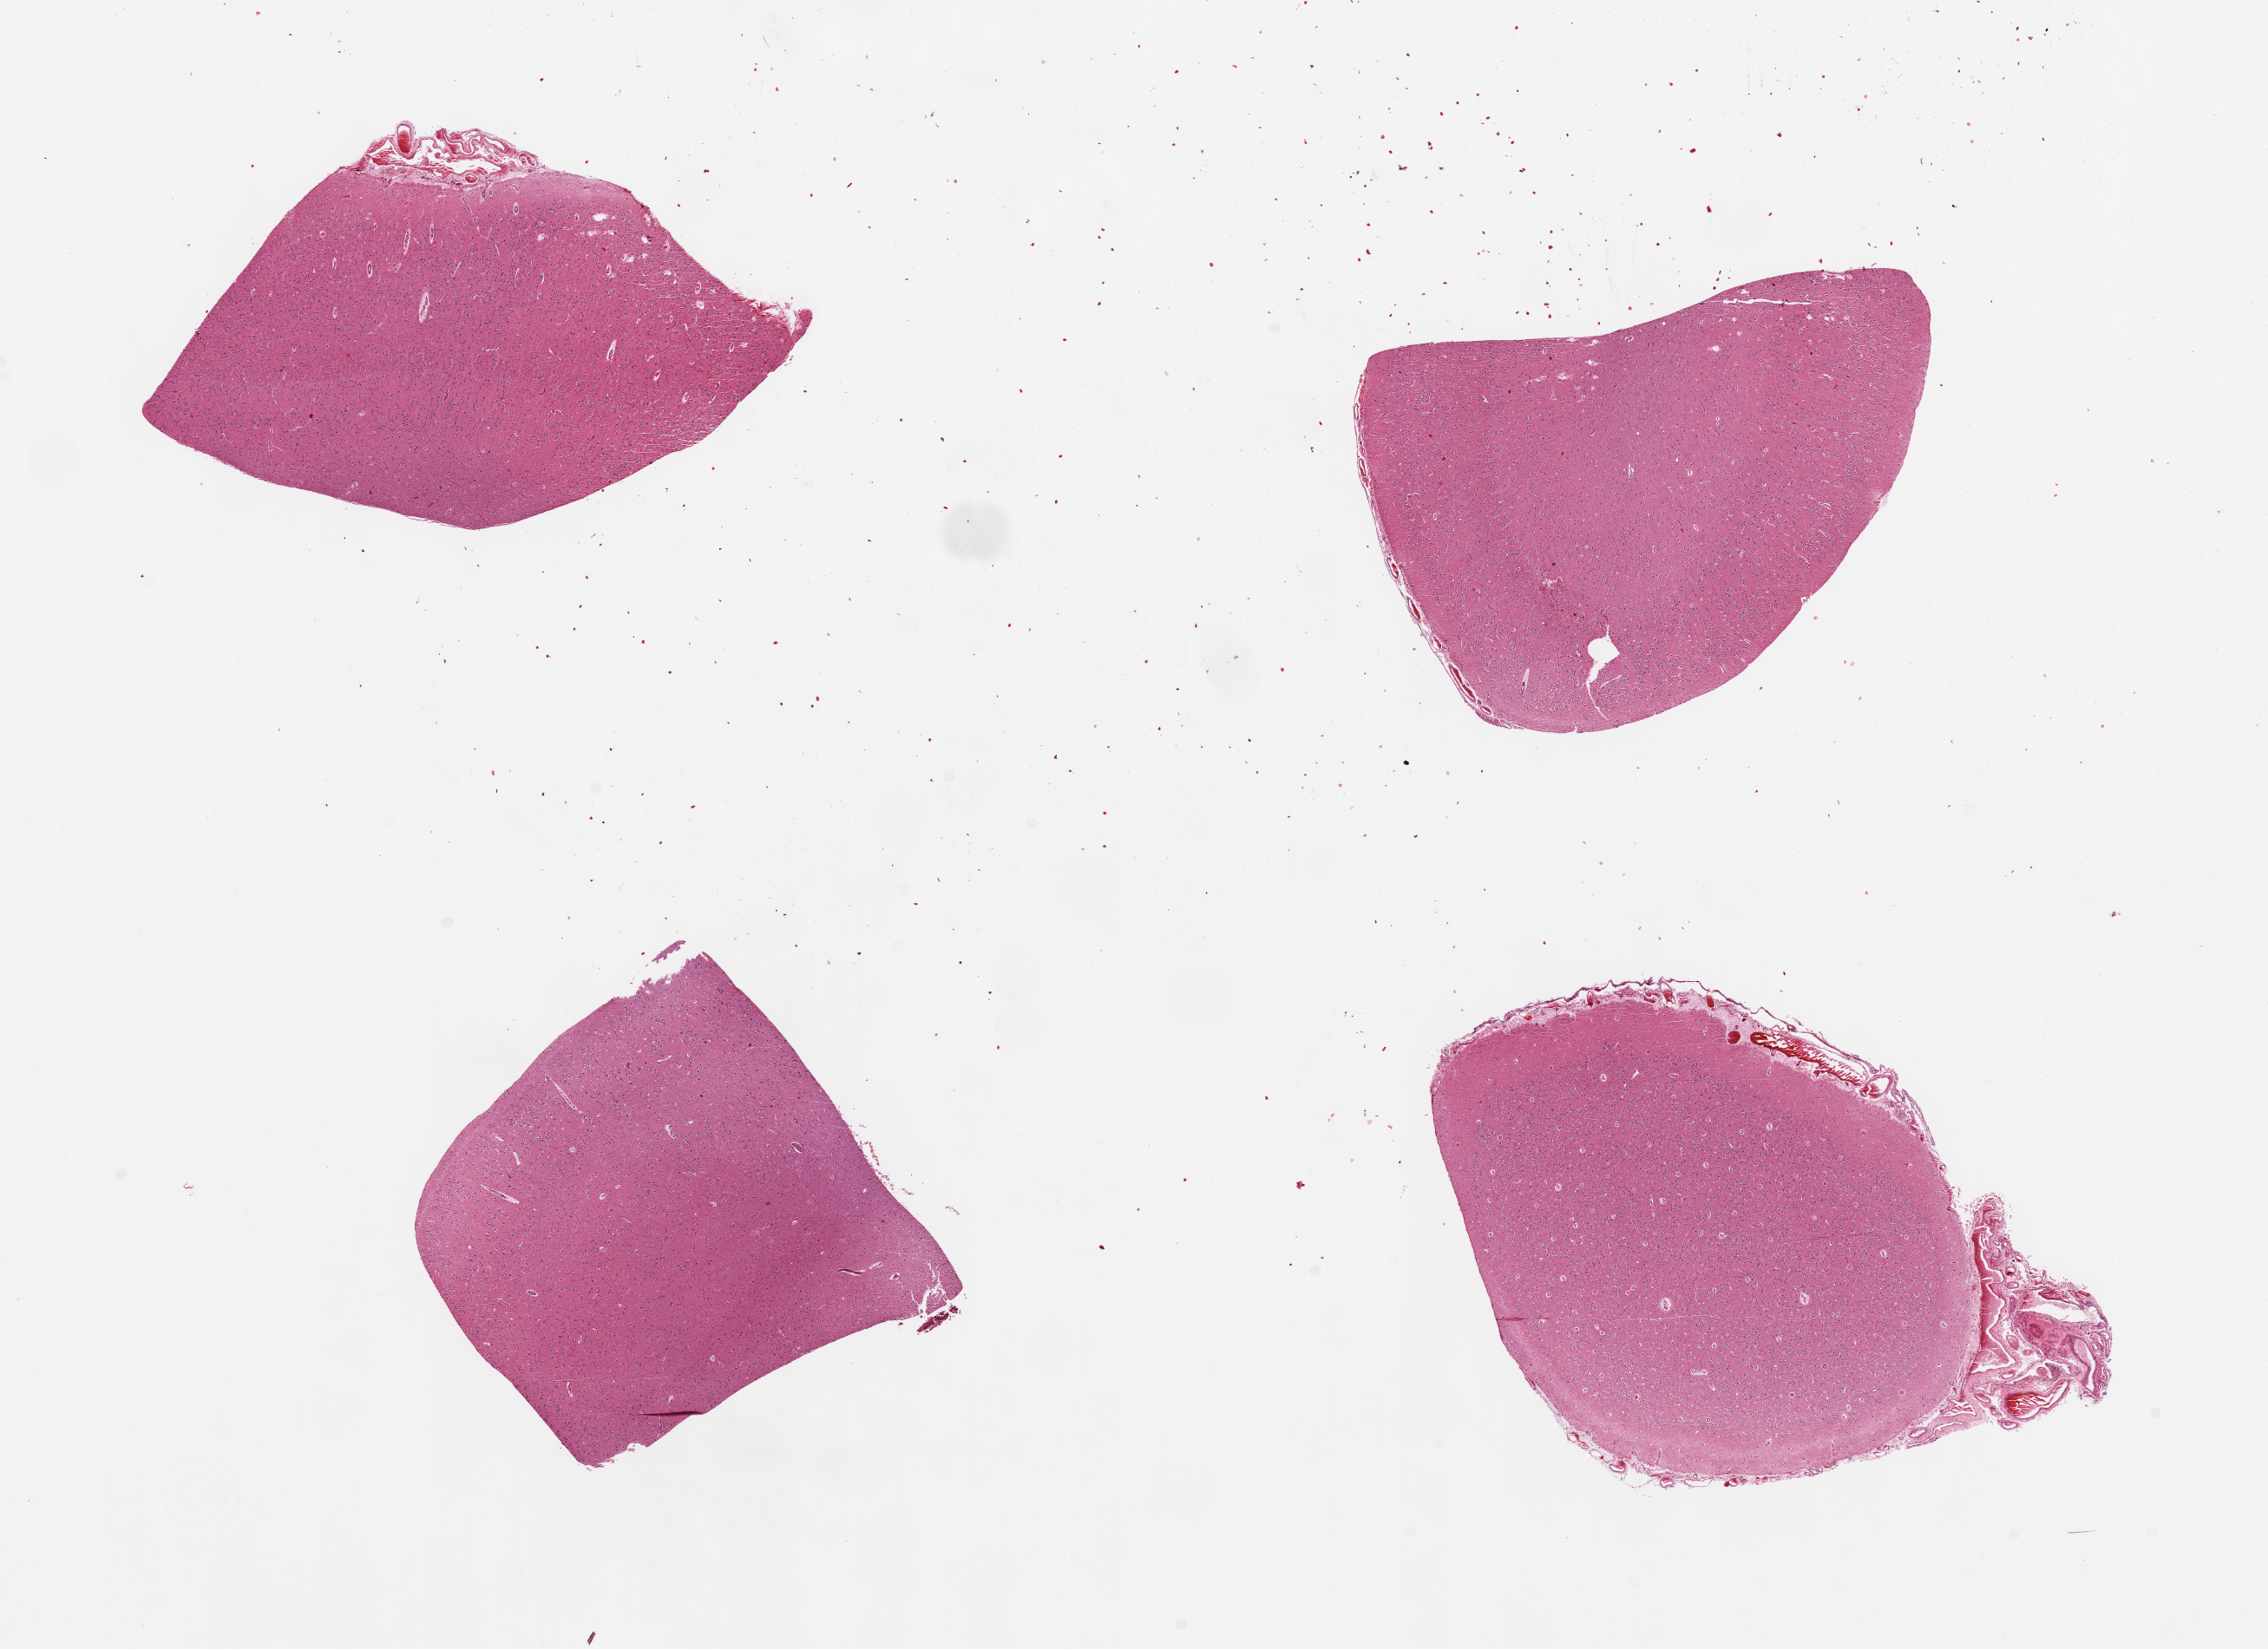
Hematoxylin and eosin (H&E) whole-slide image — shown as a low-resolution overview of the whole scanned area (about 20.7 x 15.0 mm). PAXgene-fixed paraffin-embedded (PFPE) section. Target tissue: cerebral cortex. Tissue donor sample.
Pathologist's review note for this sample: 4 pieces; congested meninges on 2 pieces.